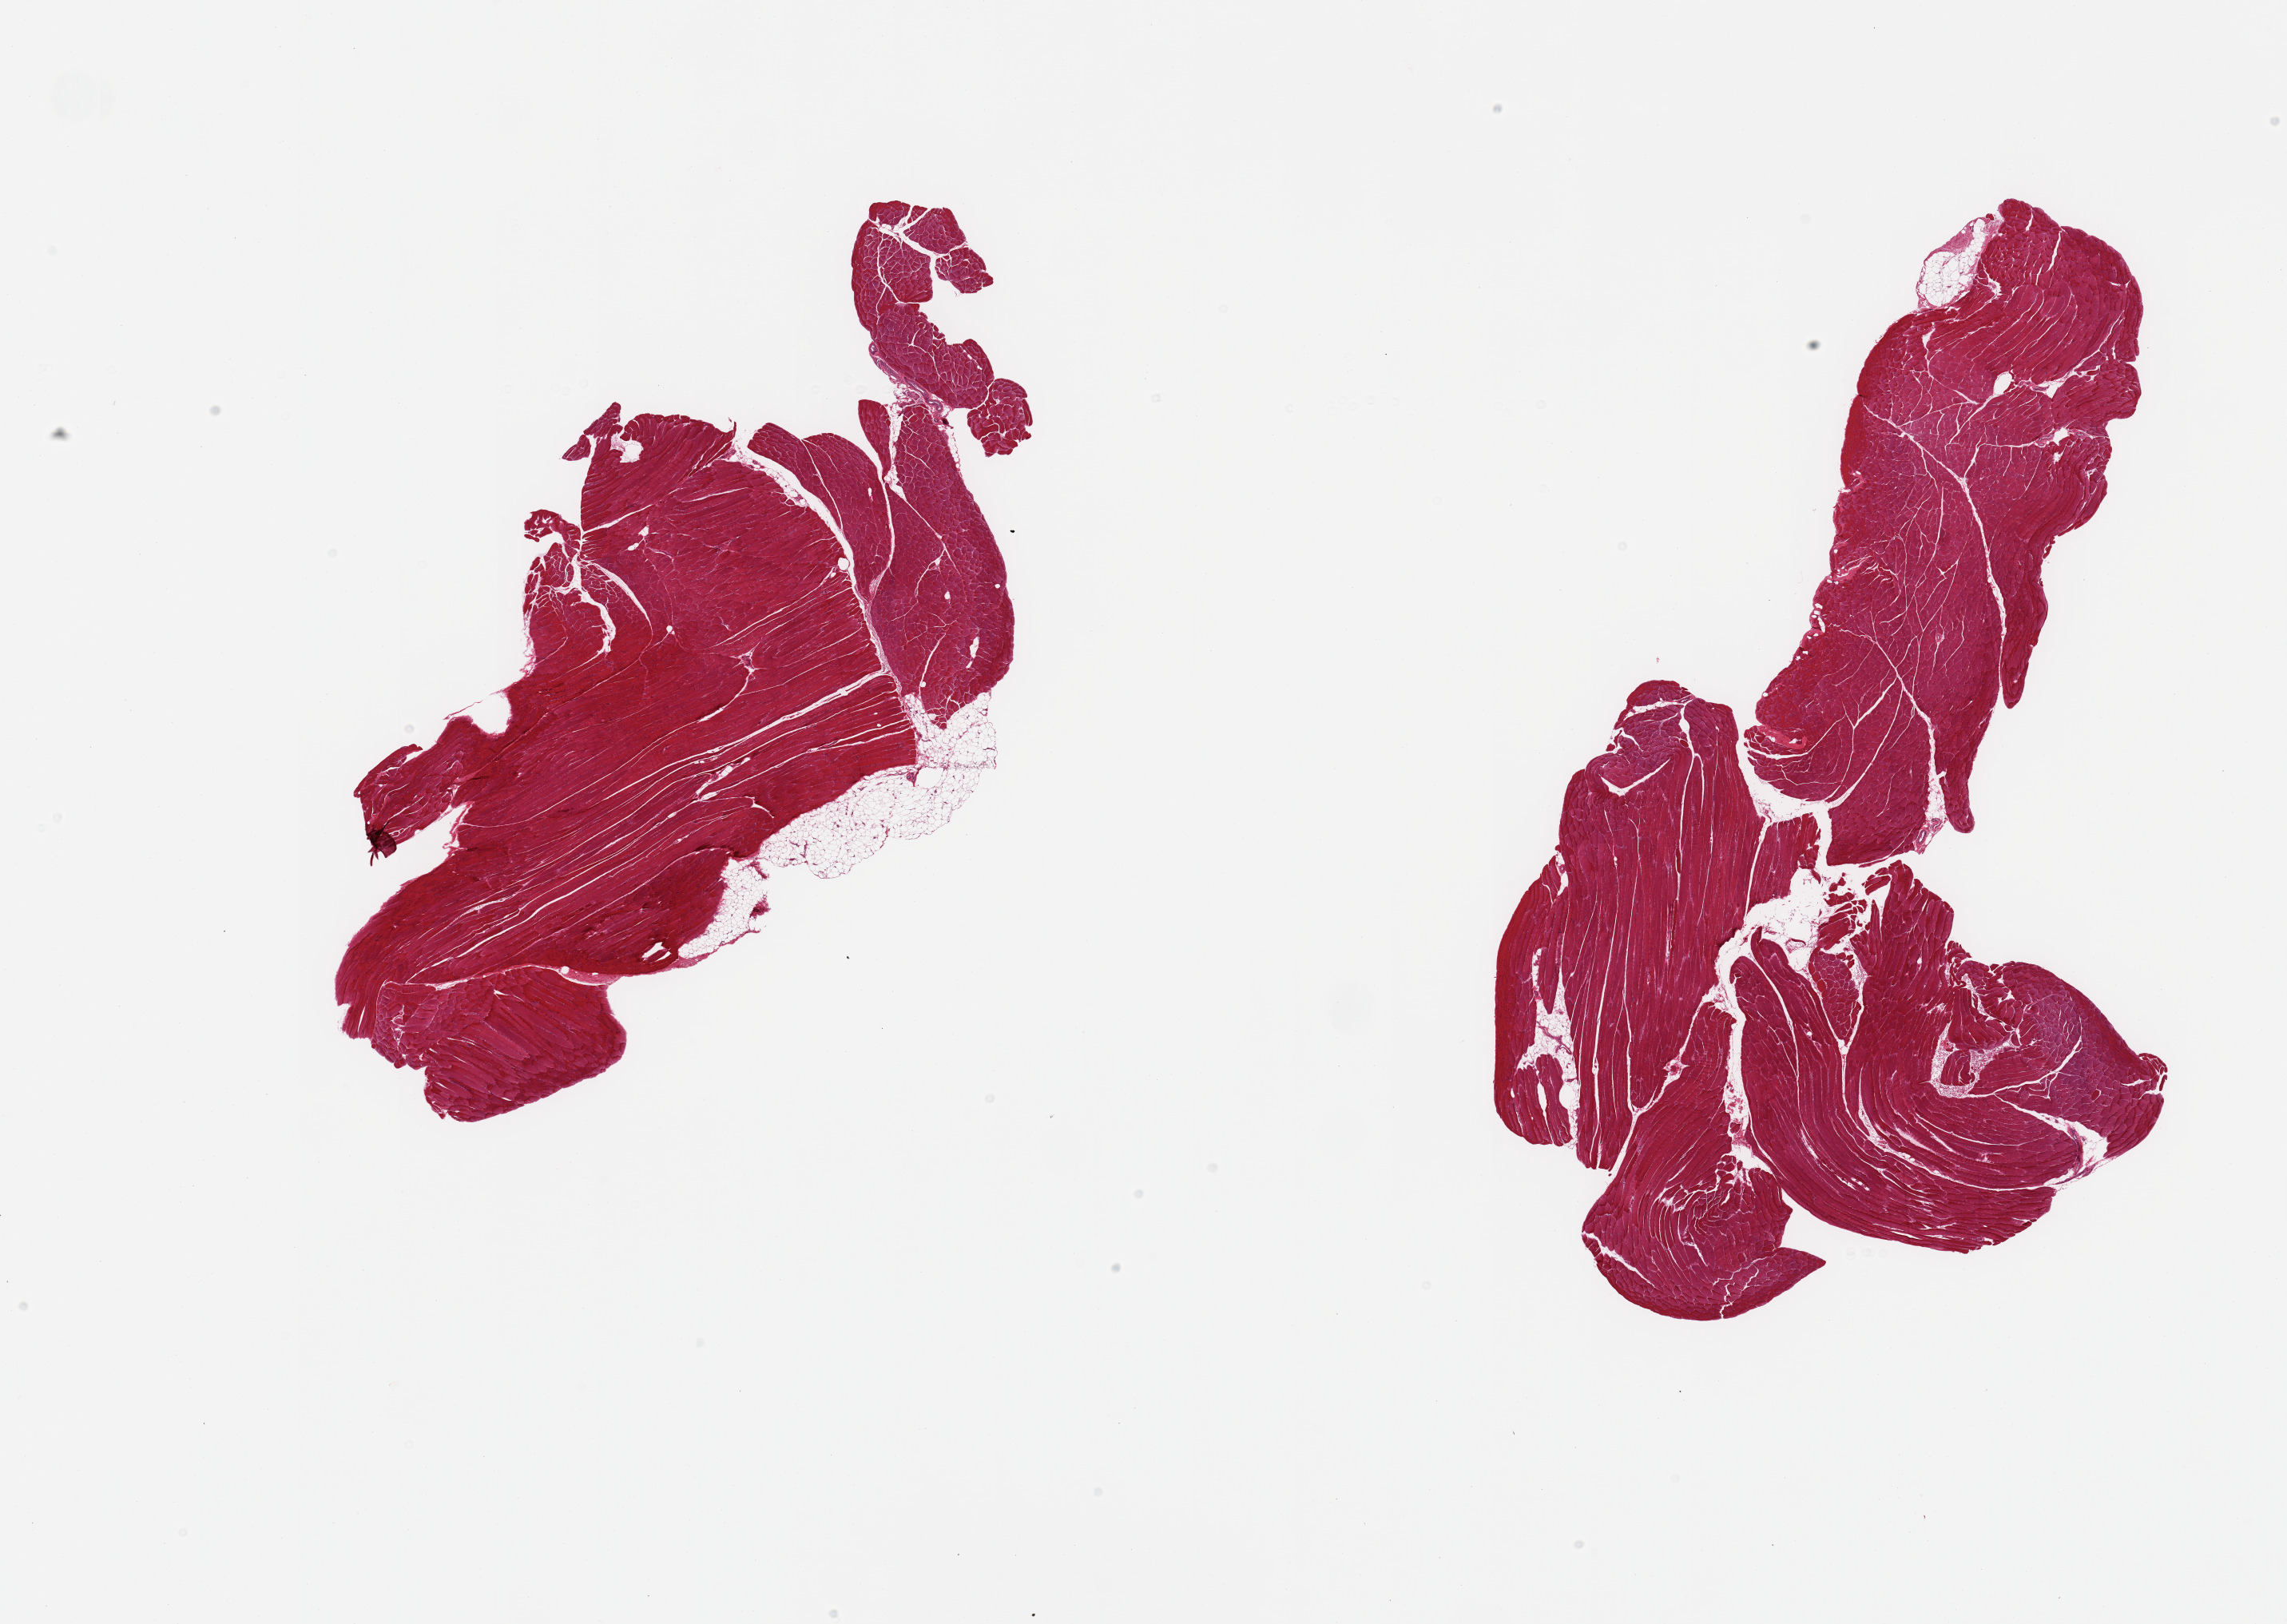
H&E whole-slide image, brightfield — whole scanned area (about 22.6 x 16.1 mm) shown as a low-resolution overview; PAXgene-fixed, paraffin-embedded tissue; sampled site (target tissue): skeletal muscle; tissue donor sample. Donor sex: female.
* pathologist's review note for this sample: 2 pieces: 10% external fat on 1